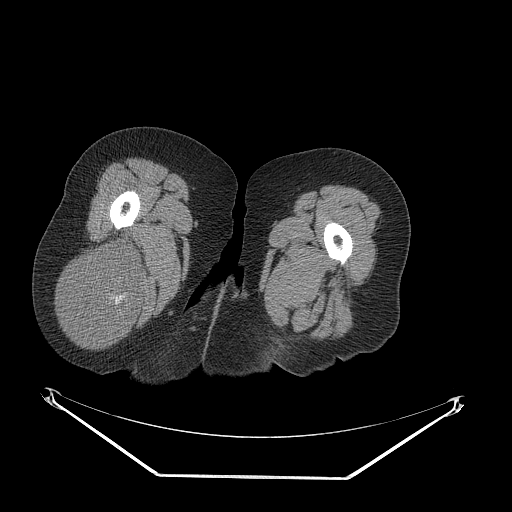
CT of an extremity soft-tissue mass (from a PET/CT study), one axial slice; slice 40 of 257 in the series (ordered by position); reconstruction kernel STANDARD; 140 kVp; soft-tissue window (W 400 / L 40 HU); 3.75 mm slice thickness; 512 × 512 image matrix, field of view 500 × 500 mm. Female patient. Case-level facts recorded for this patient, not image findings: histological type: synovial sarcoma; grade: intermediate; site of the primary tumour: right buttock.
Outlined on this slice (expert contour drawn on MRI and transferred to this co-registered scan by the dataset authors):
- gross tumour volume including surrounding oedema: bounding box [x1, y1, x2, y2] px = [62, 244, 145, 344]
- gross tumour volume (mass): [62, 244, 145, 344]